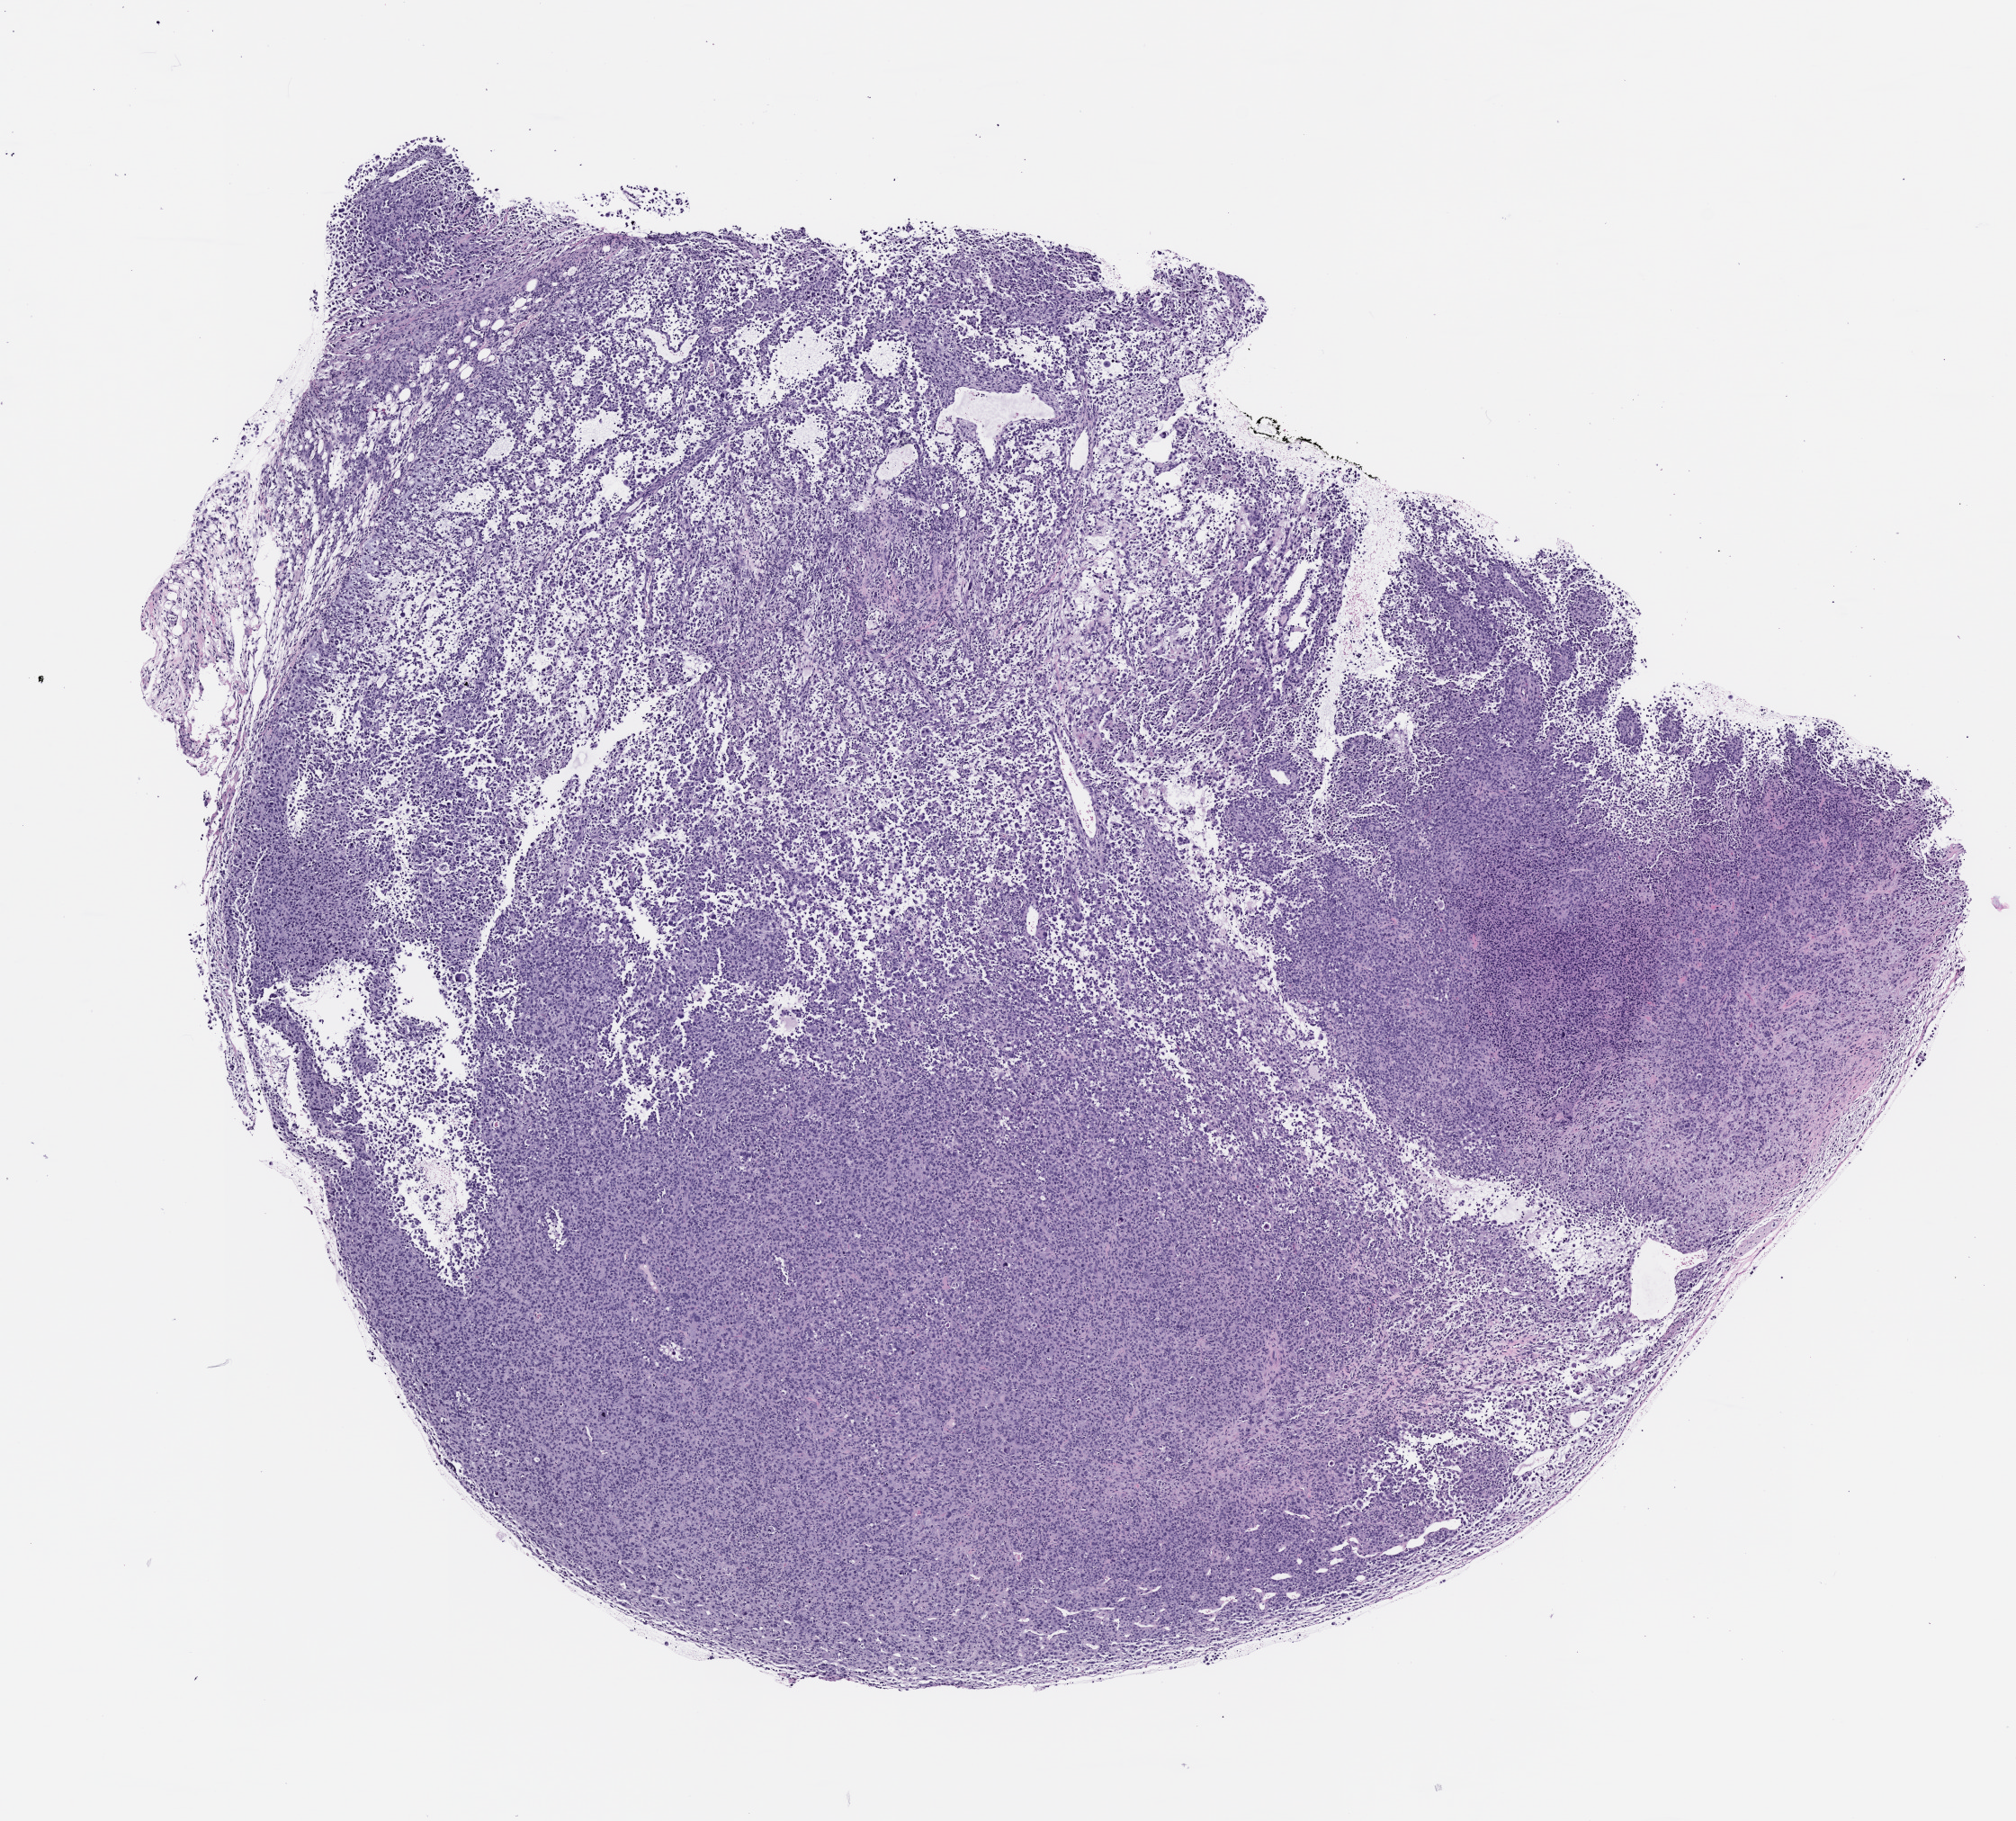
Hematoxylin and eosin (H&E) whole-slide image of a patient-derived xenograft (PDX) tumor grown in a mouse, passage 0, shown as a low-resolution overview of the whole scanned area (about 9.0 x 8.1 mm), FFPE section, tumor site category: musculoskeletal.
Originating patient diagnosis: Rhabdomyosarcoma.